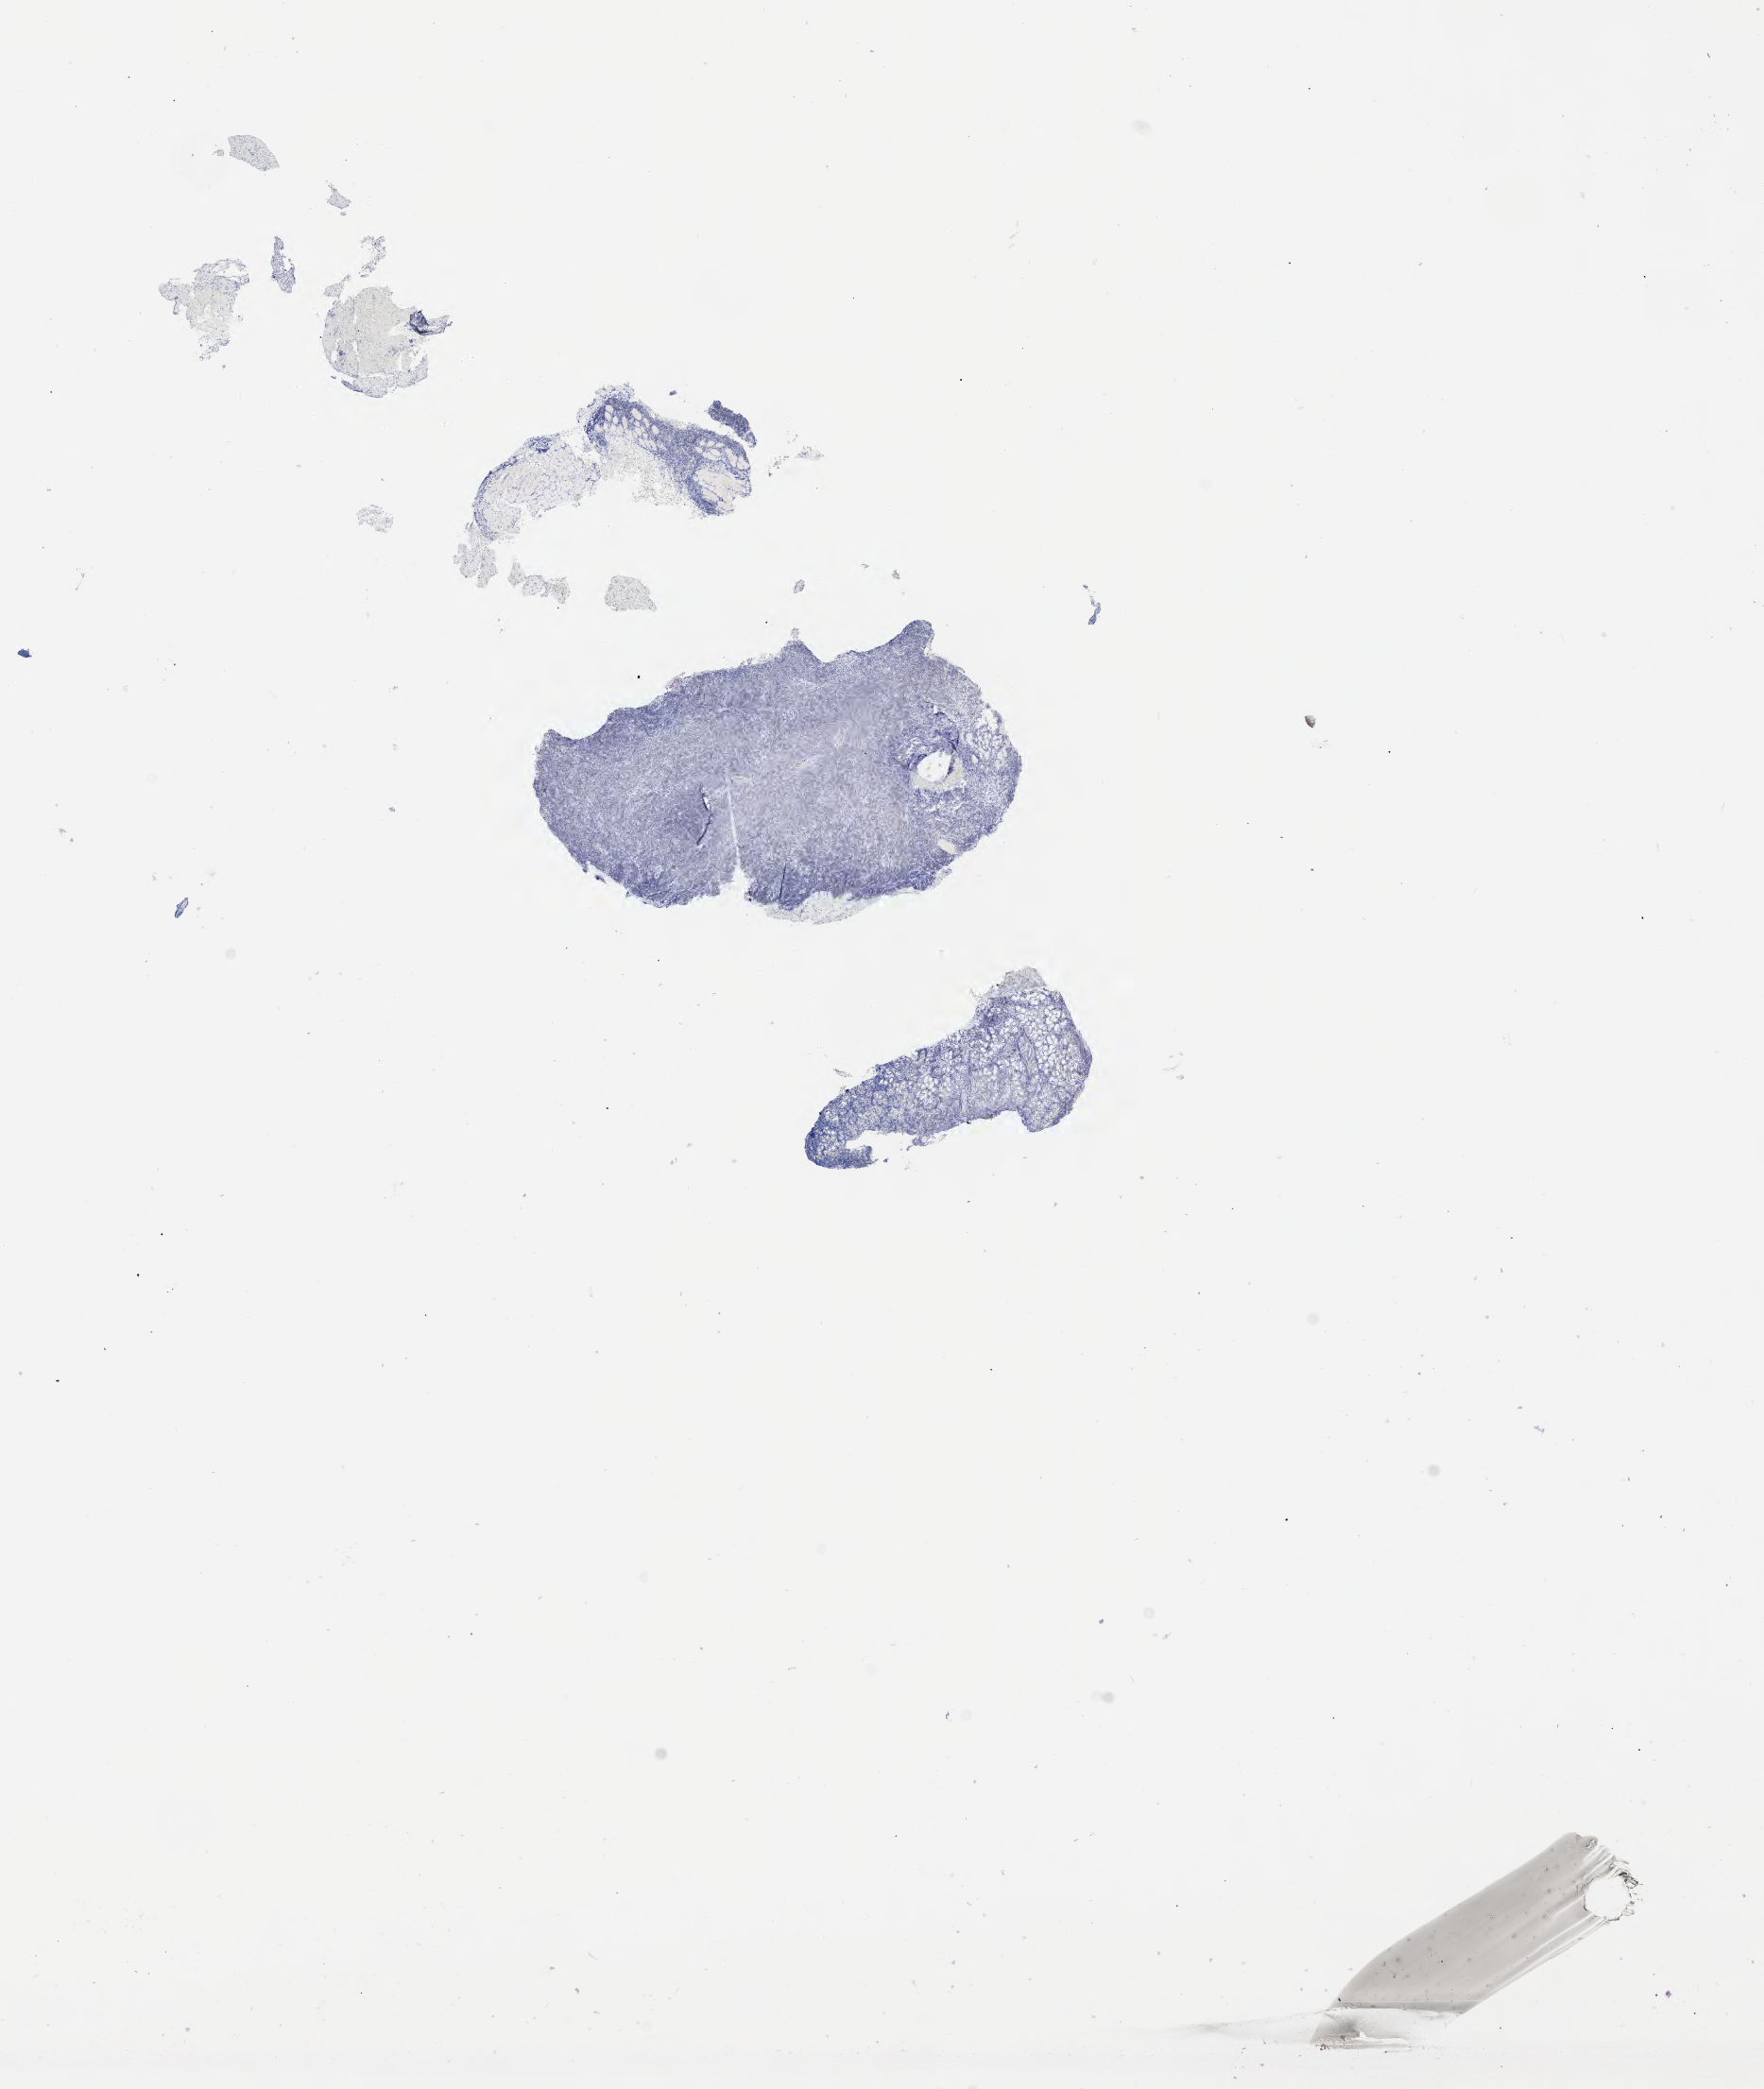
Whole-slide image, immunohistochemical stain for p53 — low-resolution overview of the scanned area, about 15.1 x 17.9 mm, specimen: tumor tissue. Male patient, 53 years old.
Histologic diagnosis: Diffuse large B-cell lymphoma, NOS.